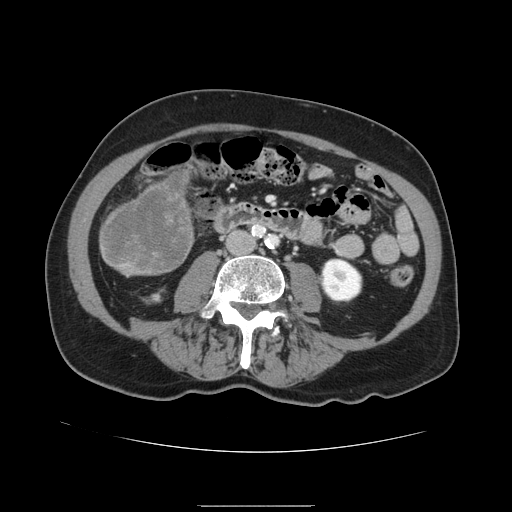
Contrast-enhanced abdominal CT, one axial slice; slice 25 of 168 in the series (ordered by position); 120 kVp; intravenous contrast given; soft-tissue window (W 400 / L 40 HU); 2.5 mm slice thickness; 512 × 512 image matrix. Male patient, age 74 years. From the clinical record (not read from this slice): diagnosis: colorectal cancer liver metastases, imaged before liver resection; multiple liver metastases: no; largest metastasis: 14.5 cm; chemotherapy before resection: no.
Structures marked on this image (expert manual segmentation):
- liver: bounding box [x1, y1, x2, y2] px = [100, 170, 194, 276]
- liver metastasis: [103, 174, 191, 271]